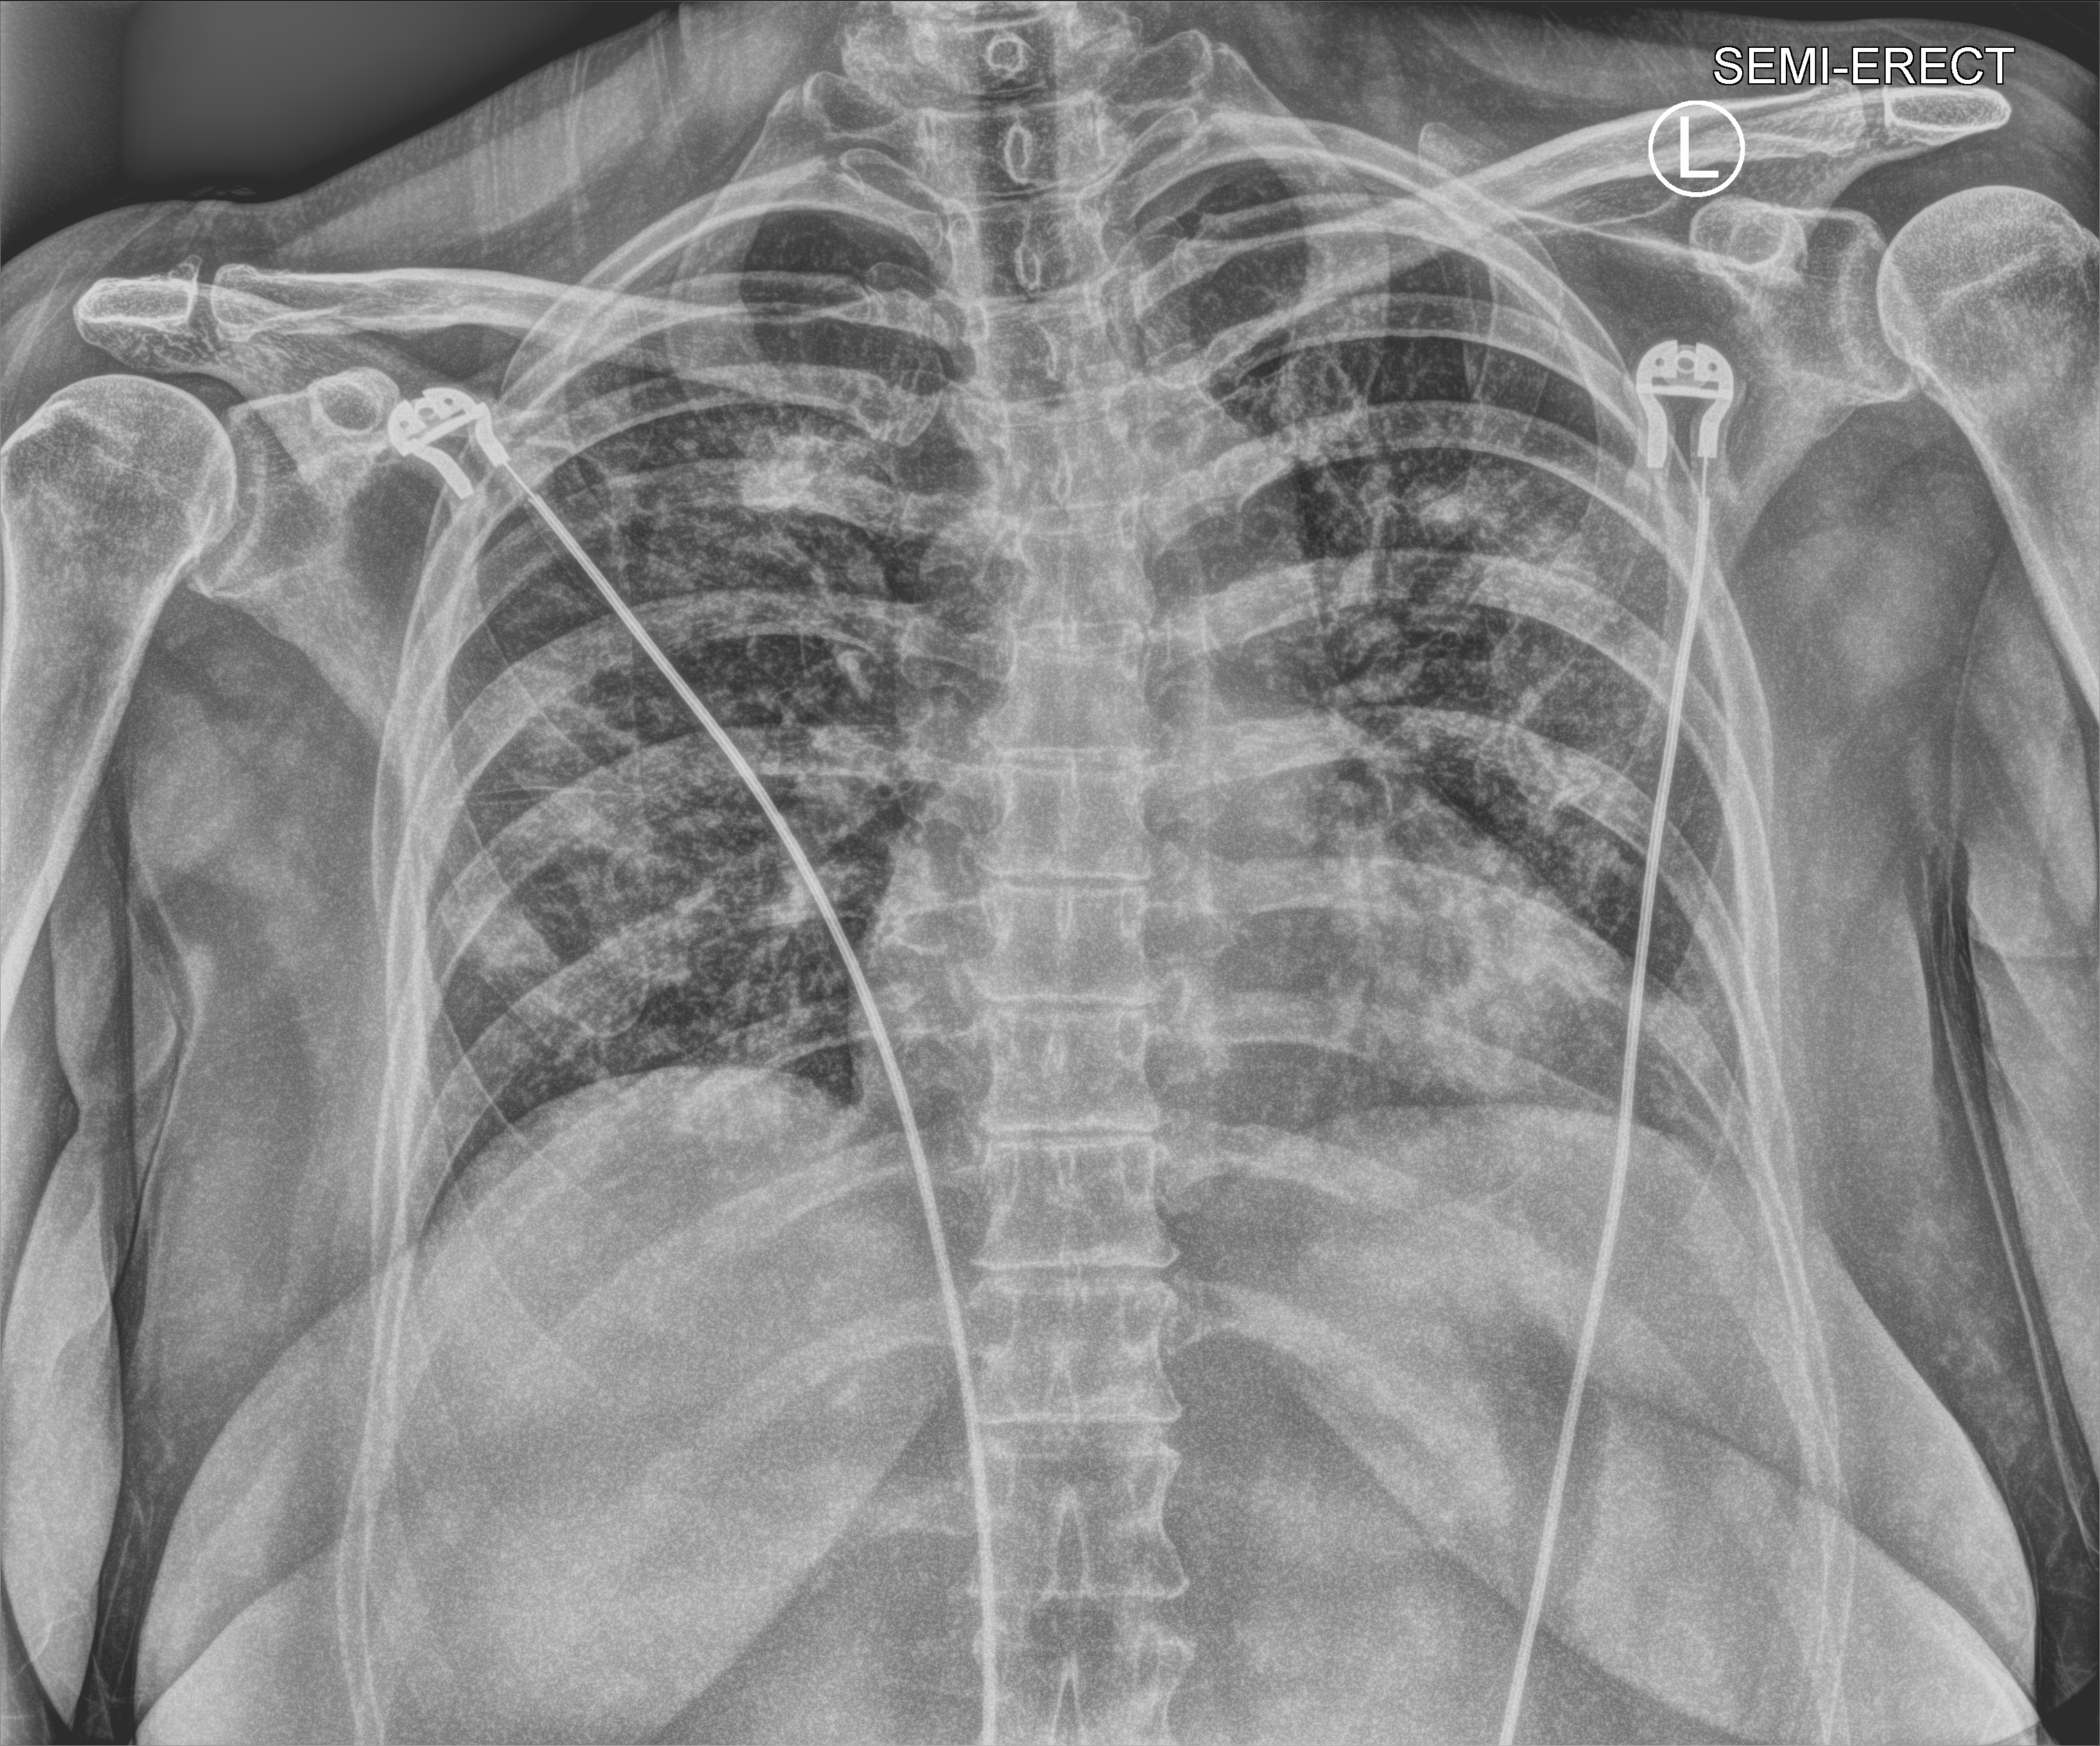
Portable chest radiograph; anteroposterior (AP) projection. Female patient hospitalised with COVID-19, age 18–59 years.
Hospital-stay facts (about this admission, not read from this image; timing relative to this image not recorded): admitted to intensive care during this hospital stay: yes; other chronic lung disease (admission record): yes; chronic kidney disease (admission record): no.